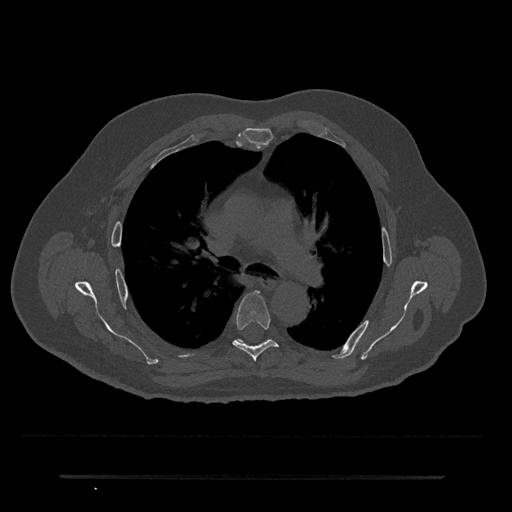
CT including the spine, one axial slice; position 479 of 797 along the scan axis; bone window (W 1800 / L 400 HU); 0.5 mm slice thickness; 512 × 512 image matrix, field of view 437 × 437 mm. Patient: male, 69 years. Case-level facts recorded for this patient, not image findings: primary cancer: prostate.
Structures marked on this image (semi-automatically segmented with operator editing):
- T5 vertebra: bounding box (x1, y1, x2, y2) in pixels: (232, 291, 278, 361)